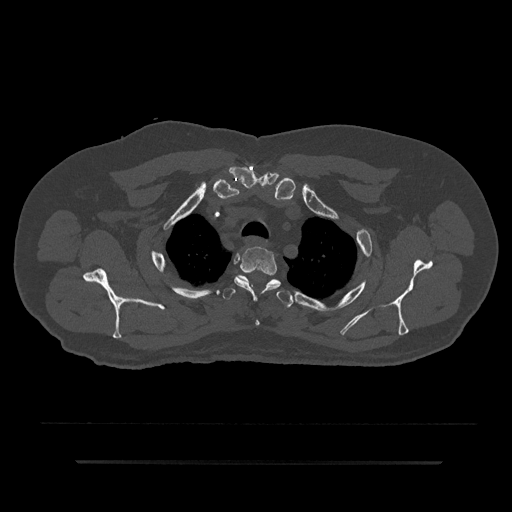
CT including the spine, one axial slice; slice 685 of 797 in the series (ordered by position); bone window (W 1800 / L 400 HU); 0.5 mm slice thickness; 512 × 512 image matrix, field of view 464 × 464 mm. Male patient, age 59 years. Case-level facts recorded for this patient, not image findings: primary cancer: bile ducts; vertebrae with lytic lesions (as recorded): T10.
Outlined on this slice (semi-automatic segmentation, software-assisted and operator-edited):
- T2 vertebra: bounding box [x1, y1, x2, y2] px = [234, 246, 281, 326]
- T3 vertebra: [223, 277, 293, 307]